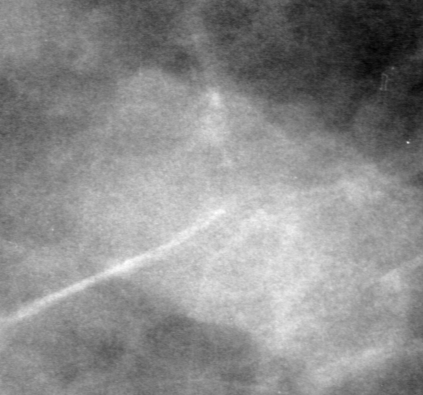
Region of interest cut from a scanned film mammogram (one marked finding), right breast, CC view.
Finding: mass, shape oval, margins obscured; BI-RADS assessment category 0 (incomplete: needs additional imaging); subtlety rating 4 on a 1 (subtle) to 5 (obvious) scale; pathology result (as recorded, not read from the image): benign.